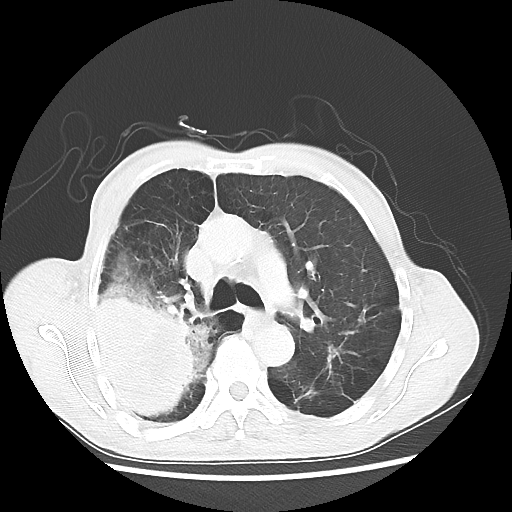
Chest CT, one axial slice; slice 35 of 58 in the series (ordered by position); reconstruction kernel LUNG; lung window (W 1500 / L -600 HU); 5 mm slice thickness; 512 × 512 image matrix, field of view 351 × 351 mm. Patient: male, 75 years. Case-level facts recorded for this patient, not image findings: clinical TNM (as recorded): T4 N1 M1.
Structures marked on this image (bounding box drawn by a radiologist):
- lung tumour (recorded histology: adenocarcinoma): bounding box <83,275,212,419> (left, top, right, bottom; pixels)